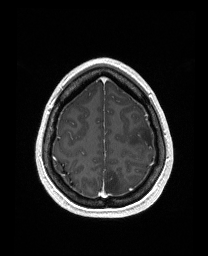
Brain MRI from a brain-tumour surgery series, one axial slice. Position 130 of 176 along the scan axis. T1-weighted post-contrast. 1 mm slice thickness. 208 × 256 image matrix. Case-level facts recorded for this patient, not image findings: histopathology: Astrocytoma; WHO grade: 3; IDH mutation: yes.
Outlined on this slice (manually delineated by an expert):
- tumour: bounding box (x1, y1, x2, y2) in pixels: (129, 124, 155, 148)